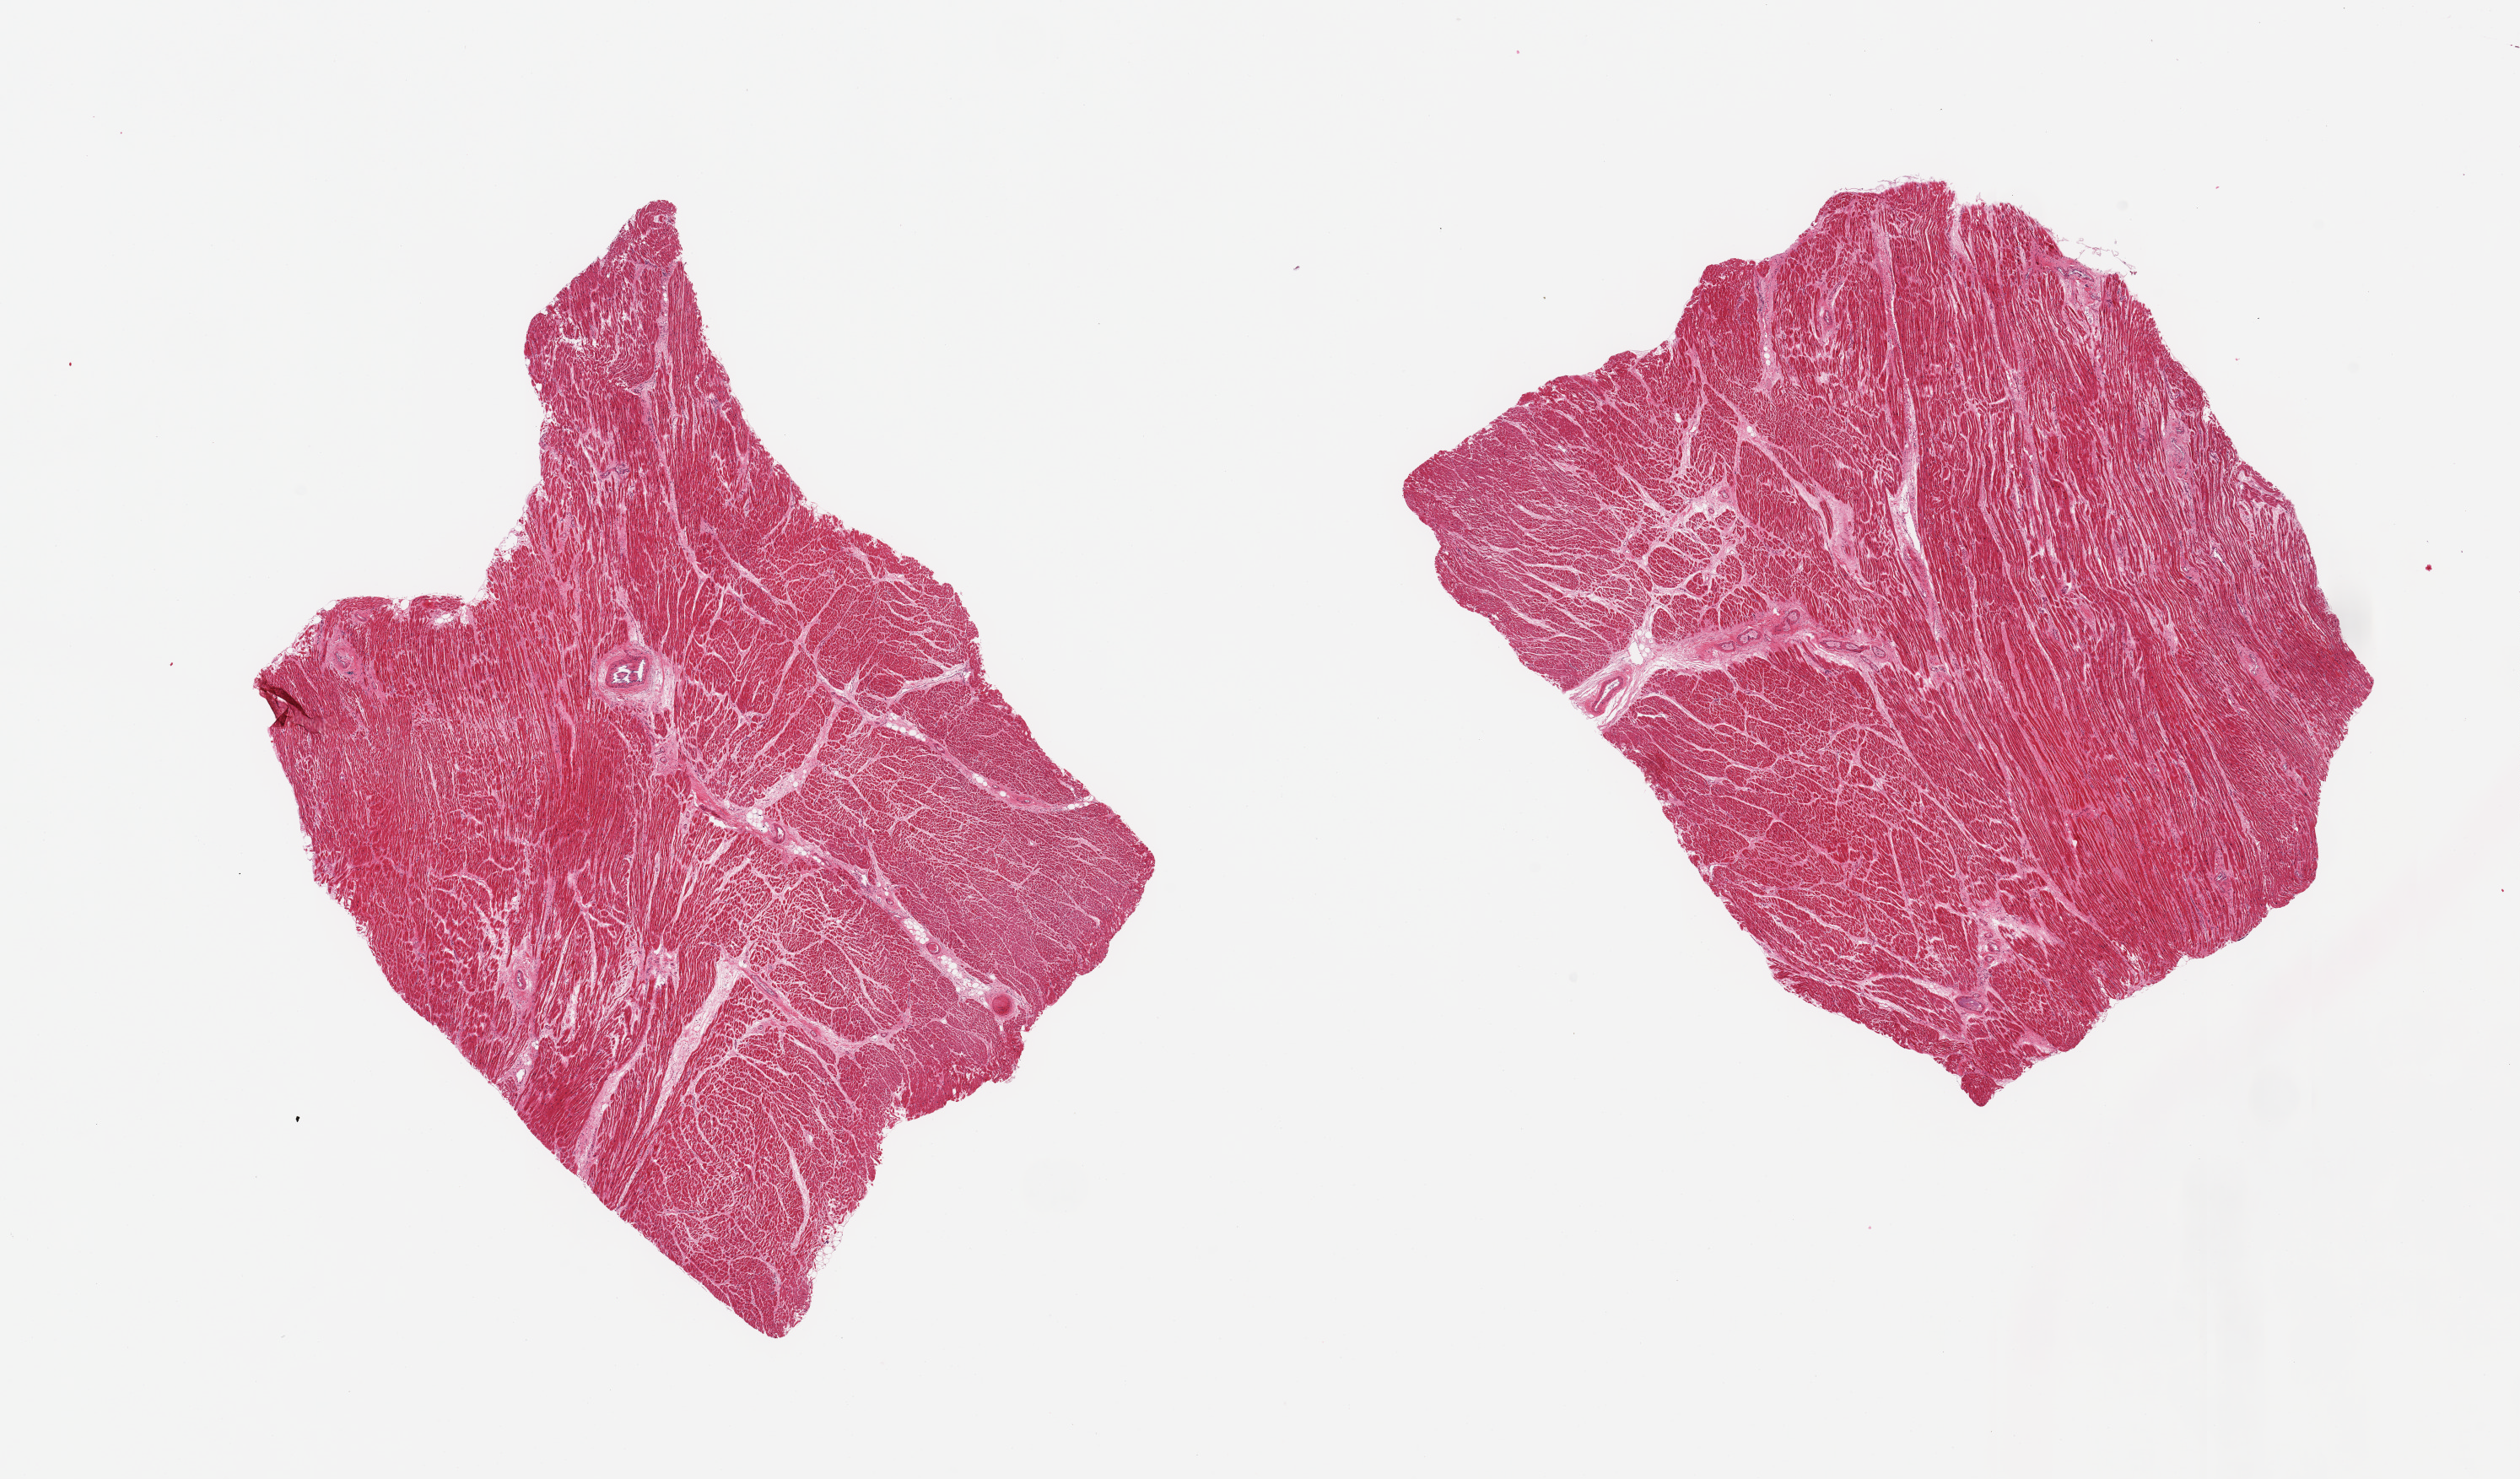
H&E whole-slide image — whole scanned area (about 23.6 x 13.9 mm) shown as a low-resolution overview. PAXgene-fixed paraffin-embedded (PFPE) section. Section of heart (target tissue). Tissue donor sample.
• review note (as recorded): 2 pieces; 20% area of interstitial congestion & hemorrhage in 1 piece, possible early infarct